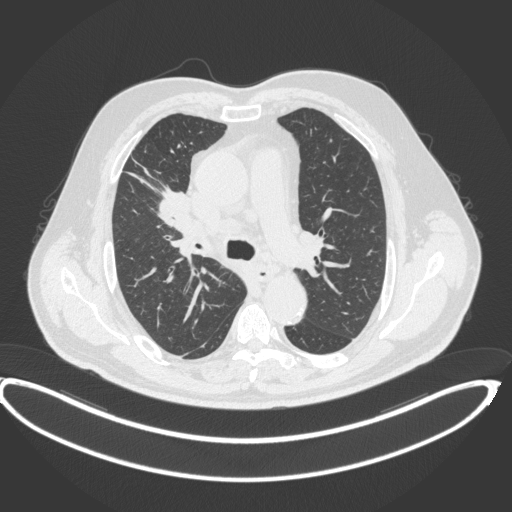
Chest CT, one axial slice. Slice 270 of 395 in the series (ordered by position). Reconstruction kernel B31f. 120 kVp. Lung window (W 1500 / L -600 HU). 512 × 512 image matrix. Patient: male, 62 years. Case-level facts recorded for this patient, not image findings: clinical TNM (as recorded): T1c N3 M1c.
Structures marked on this image (bounding box drawn by a radiologist):
- lung tumour (recorded histology: adenocarcinoma): bounding box (x1, y1, x2, y2) in pixels: (155, 184, 195, 236)